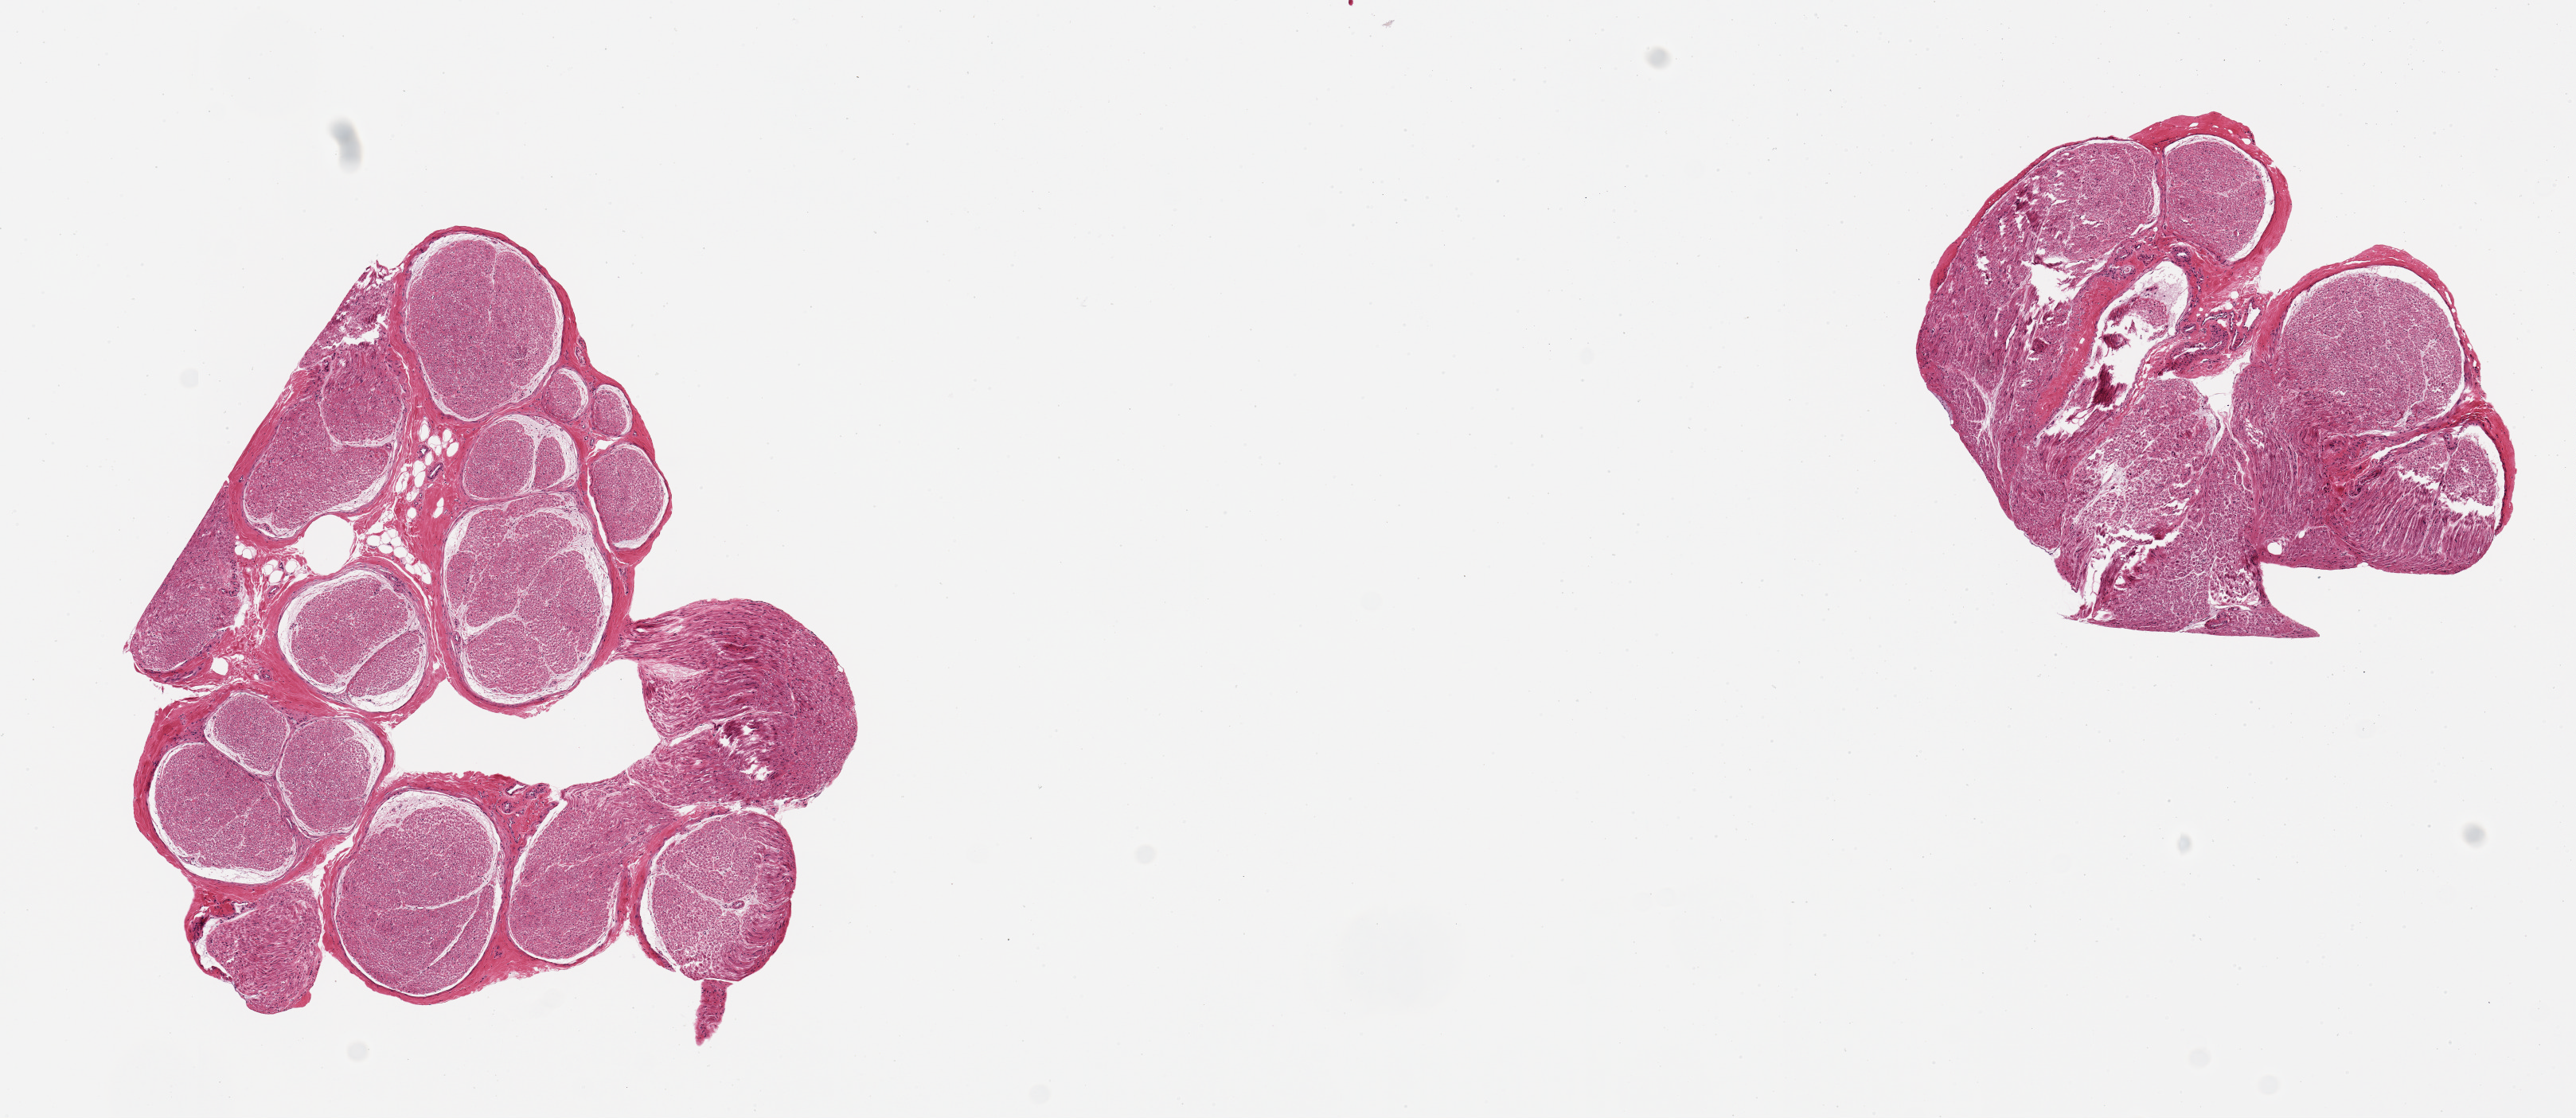
Whole-slide image, H&E stain, a low-resolution overview of the entire scanned area, about 12.8 x 5.6 mm. PAXgene-fixed, paraffin-embedded tissue. Sampled site (target tissue): tibial nerve. Tissue donor sample. Donor sex: male.
Reviewer comment on this tissue sample: 2 pieces, 4x4 & 3x2.5mm; good clean aliquots.